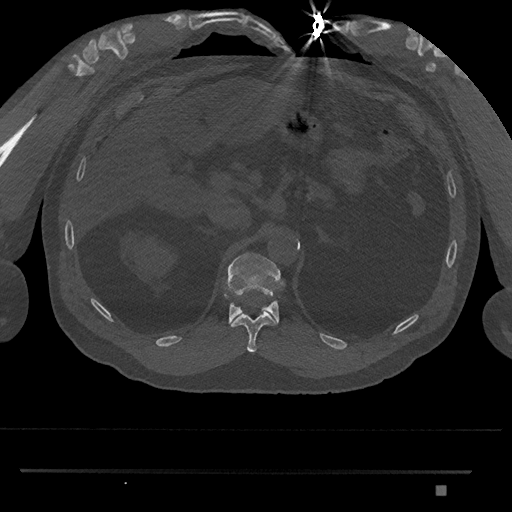
CT including the spine, one axial slice. Slice 920 of 1134 in the series (ordered by position). Reconstruction kernel Br40s/3. 120 kVp. Bone window (W 1800 / L 400 HU). 0.5 mm slice thickness. 512 × 512 image matrix. Patient: male, 65 years. Case-level facts recorded for this patient, not image findings: primary cancer: prostate.
Annotated regions visible in this slice (semi-automatic segmentation, software-assisted and operator-edited):
- T11 vertebra: bounding box (x1, y1, x2, y2) in pixels: (231, 312, 277, 353)
- T12 vertebra: (223, 252, 284, 324)